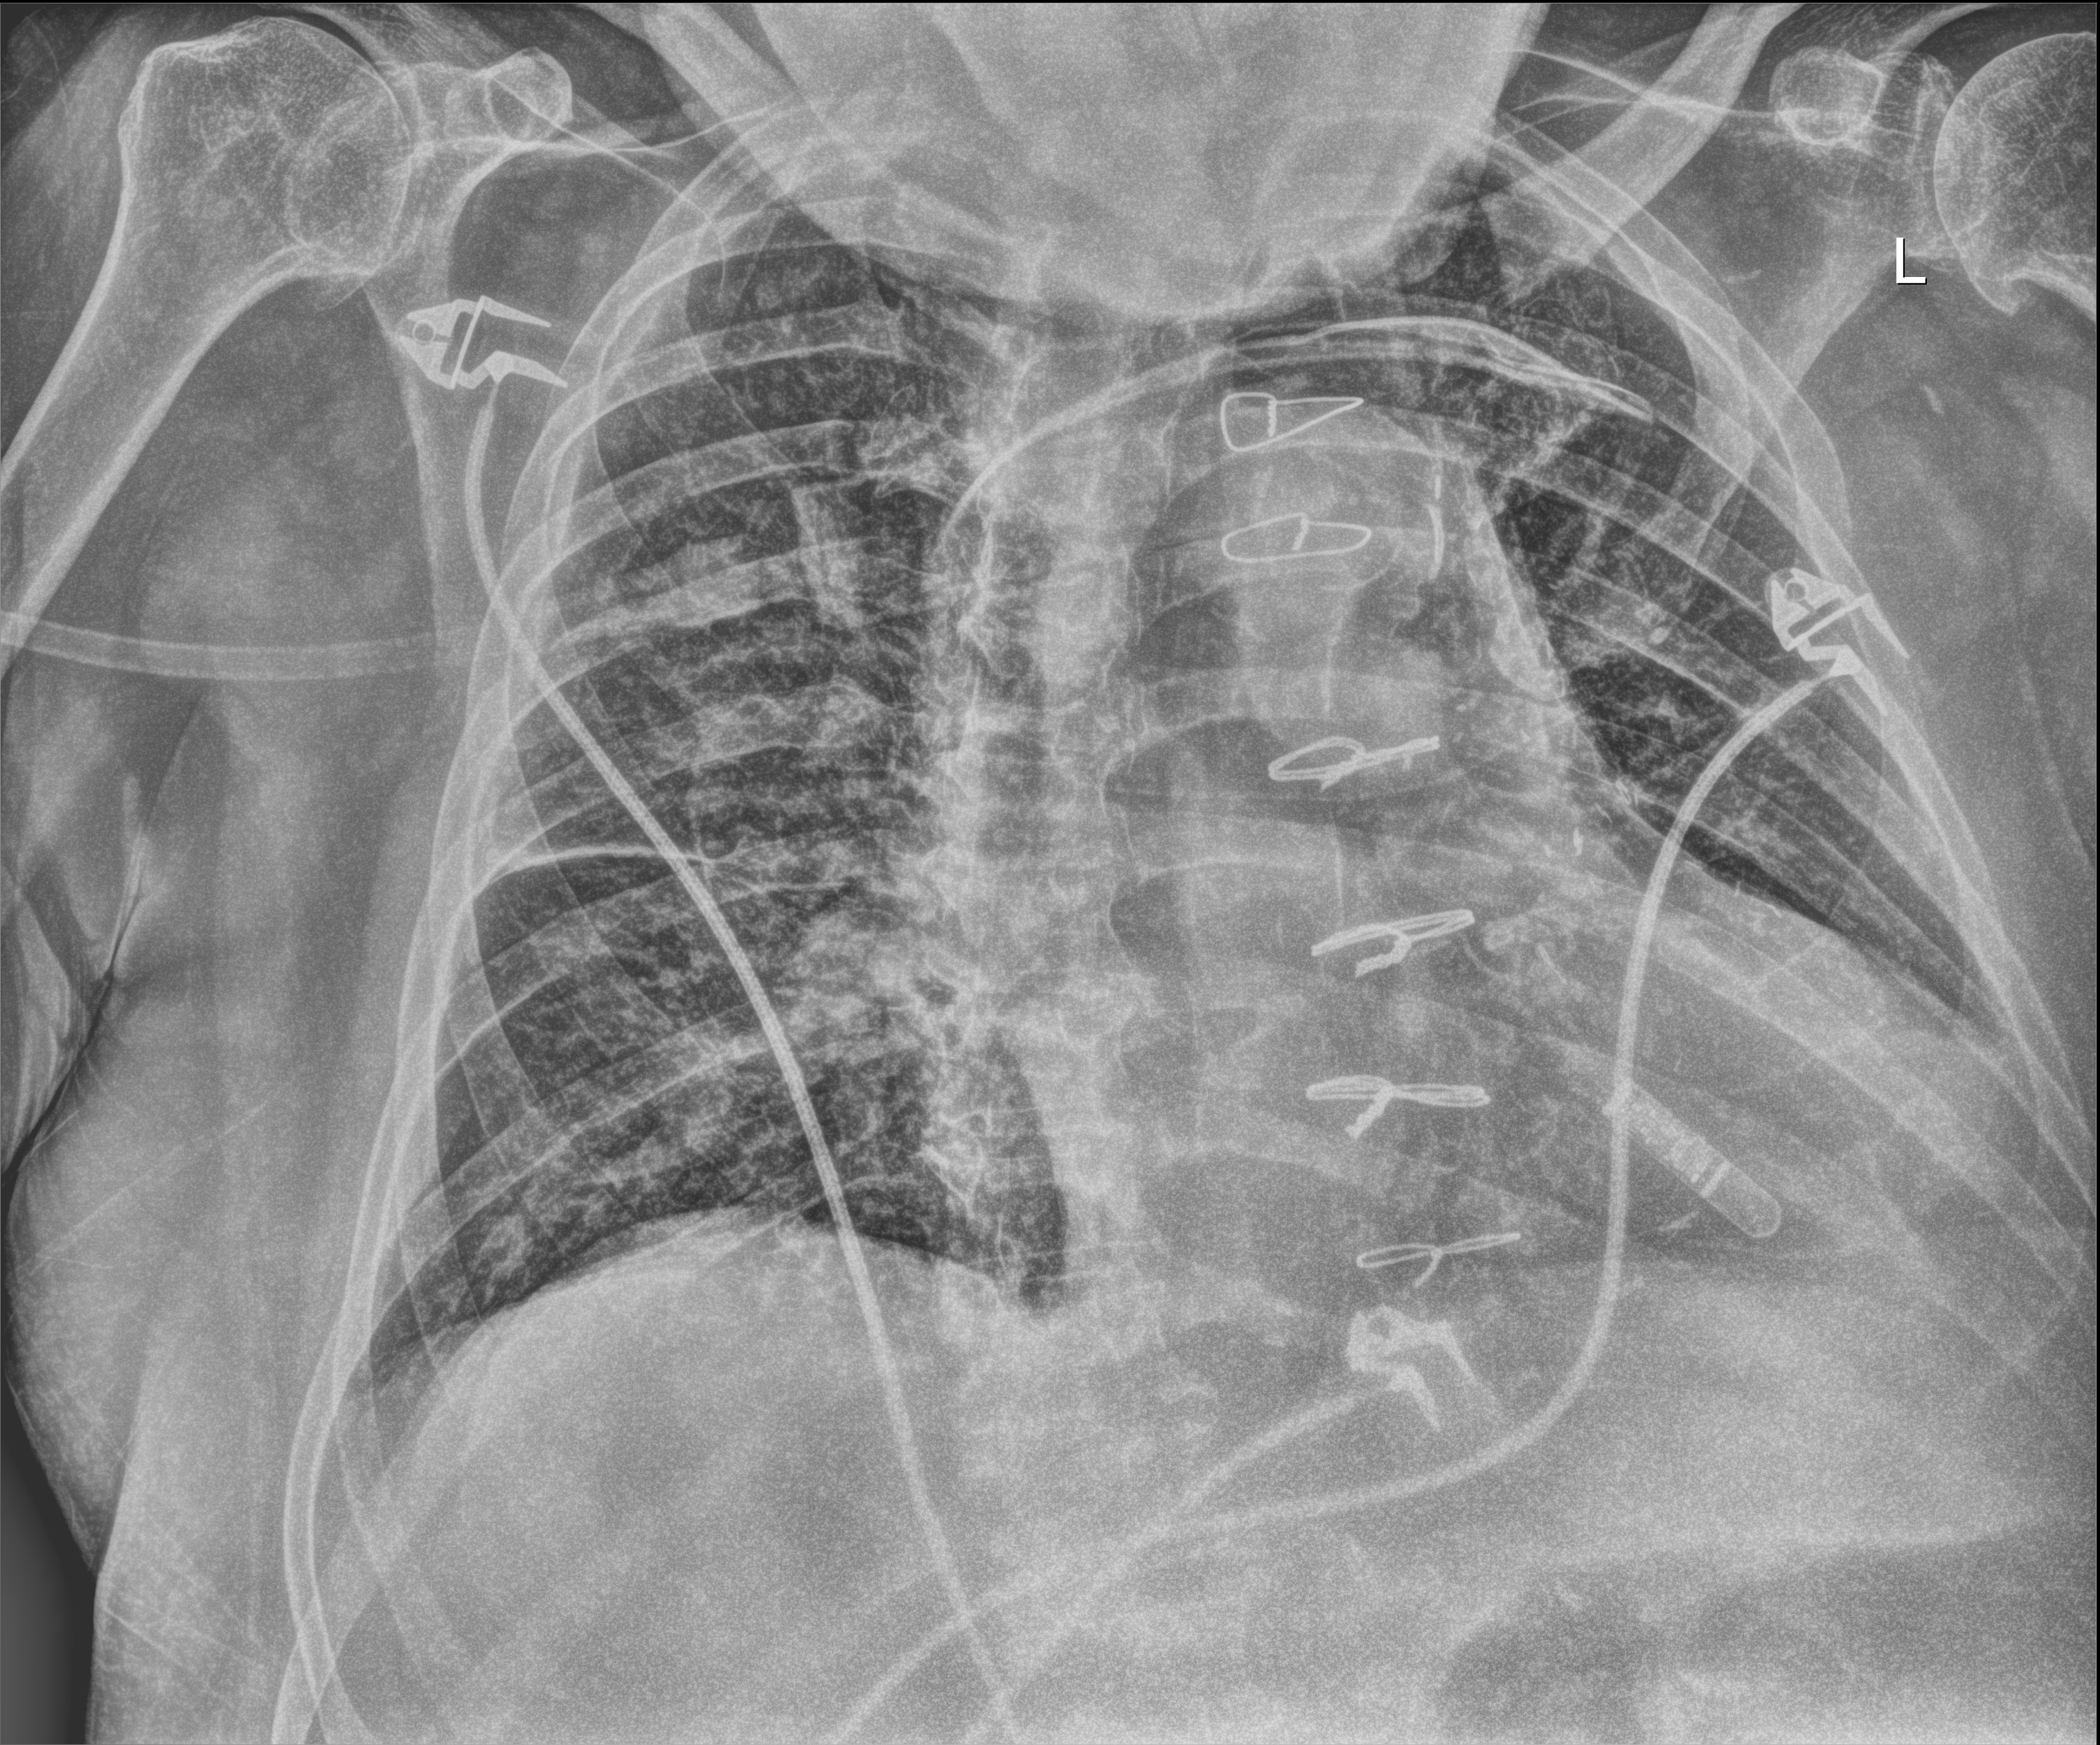
Chest X-ray (portable); anteroposterior (AP) projection. Male patient hospitalised with COVID-19, age 60–74 years.
Admission-level facts for this patient (not findings on this image; timing relative to this image not recorded): admitted to intensive care during this hospital stay: no.